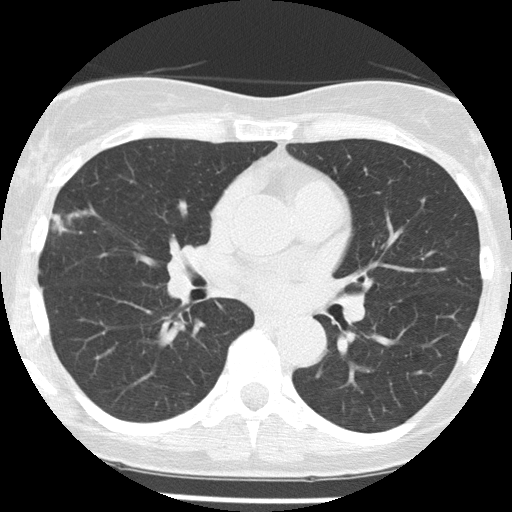
Low-dose screening chest CT, one axial slice; position 86 of 156 along the scan axis; reconstruction kernel FC51; lung window (W 1500 / L -600 HU); 2 mm slice thickness; 512 × 512 image matrix.
Annotated regions visible in this slice (outlined manually by an expert reader):
- lesion 1 (tumor, middle lobe of right lung): bounding box <51,214,67,235> (left, top, right, bottom; pixels)